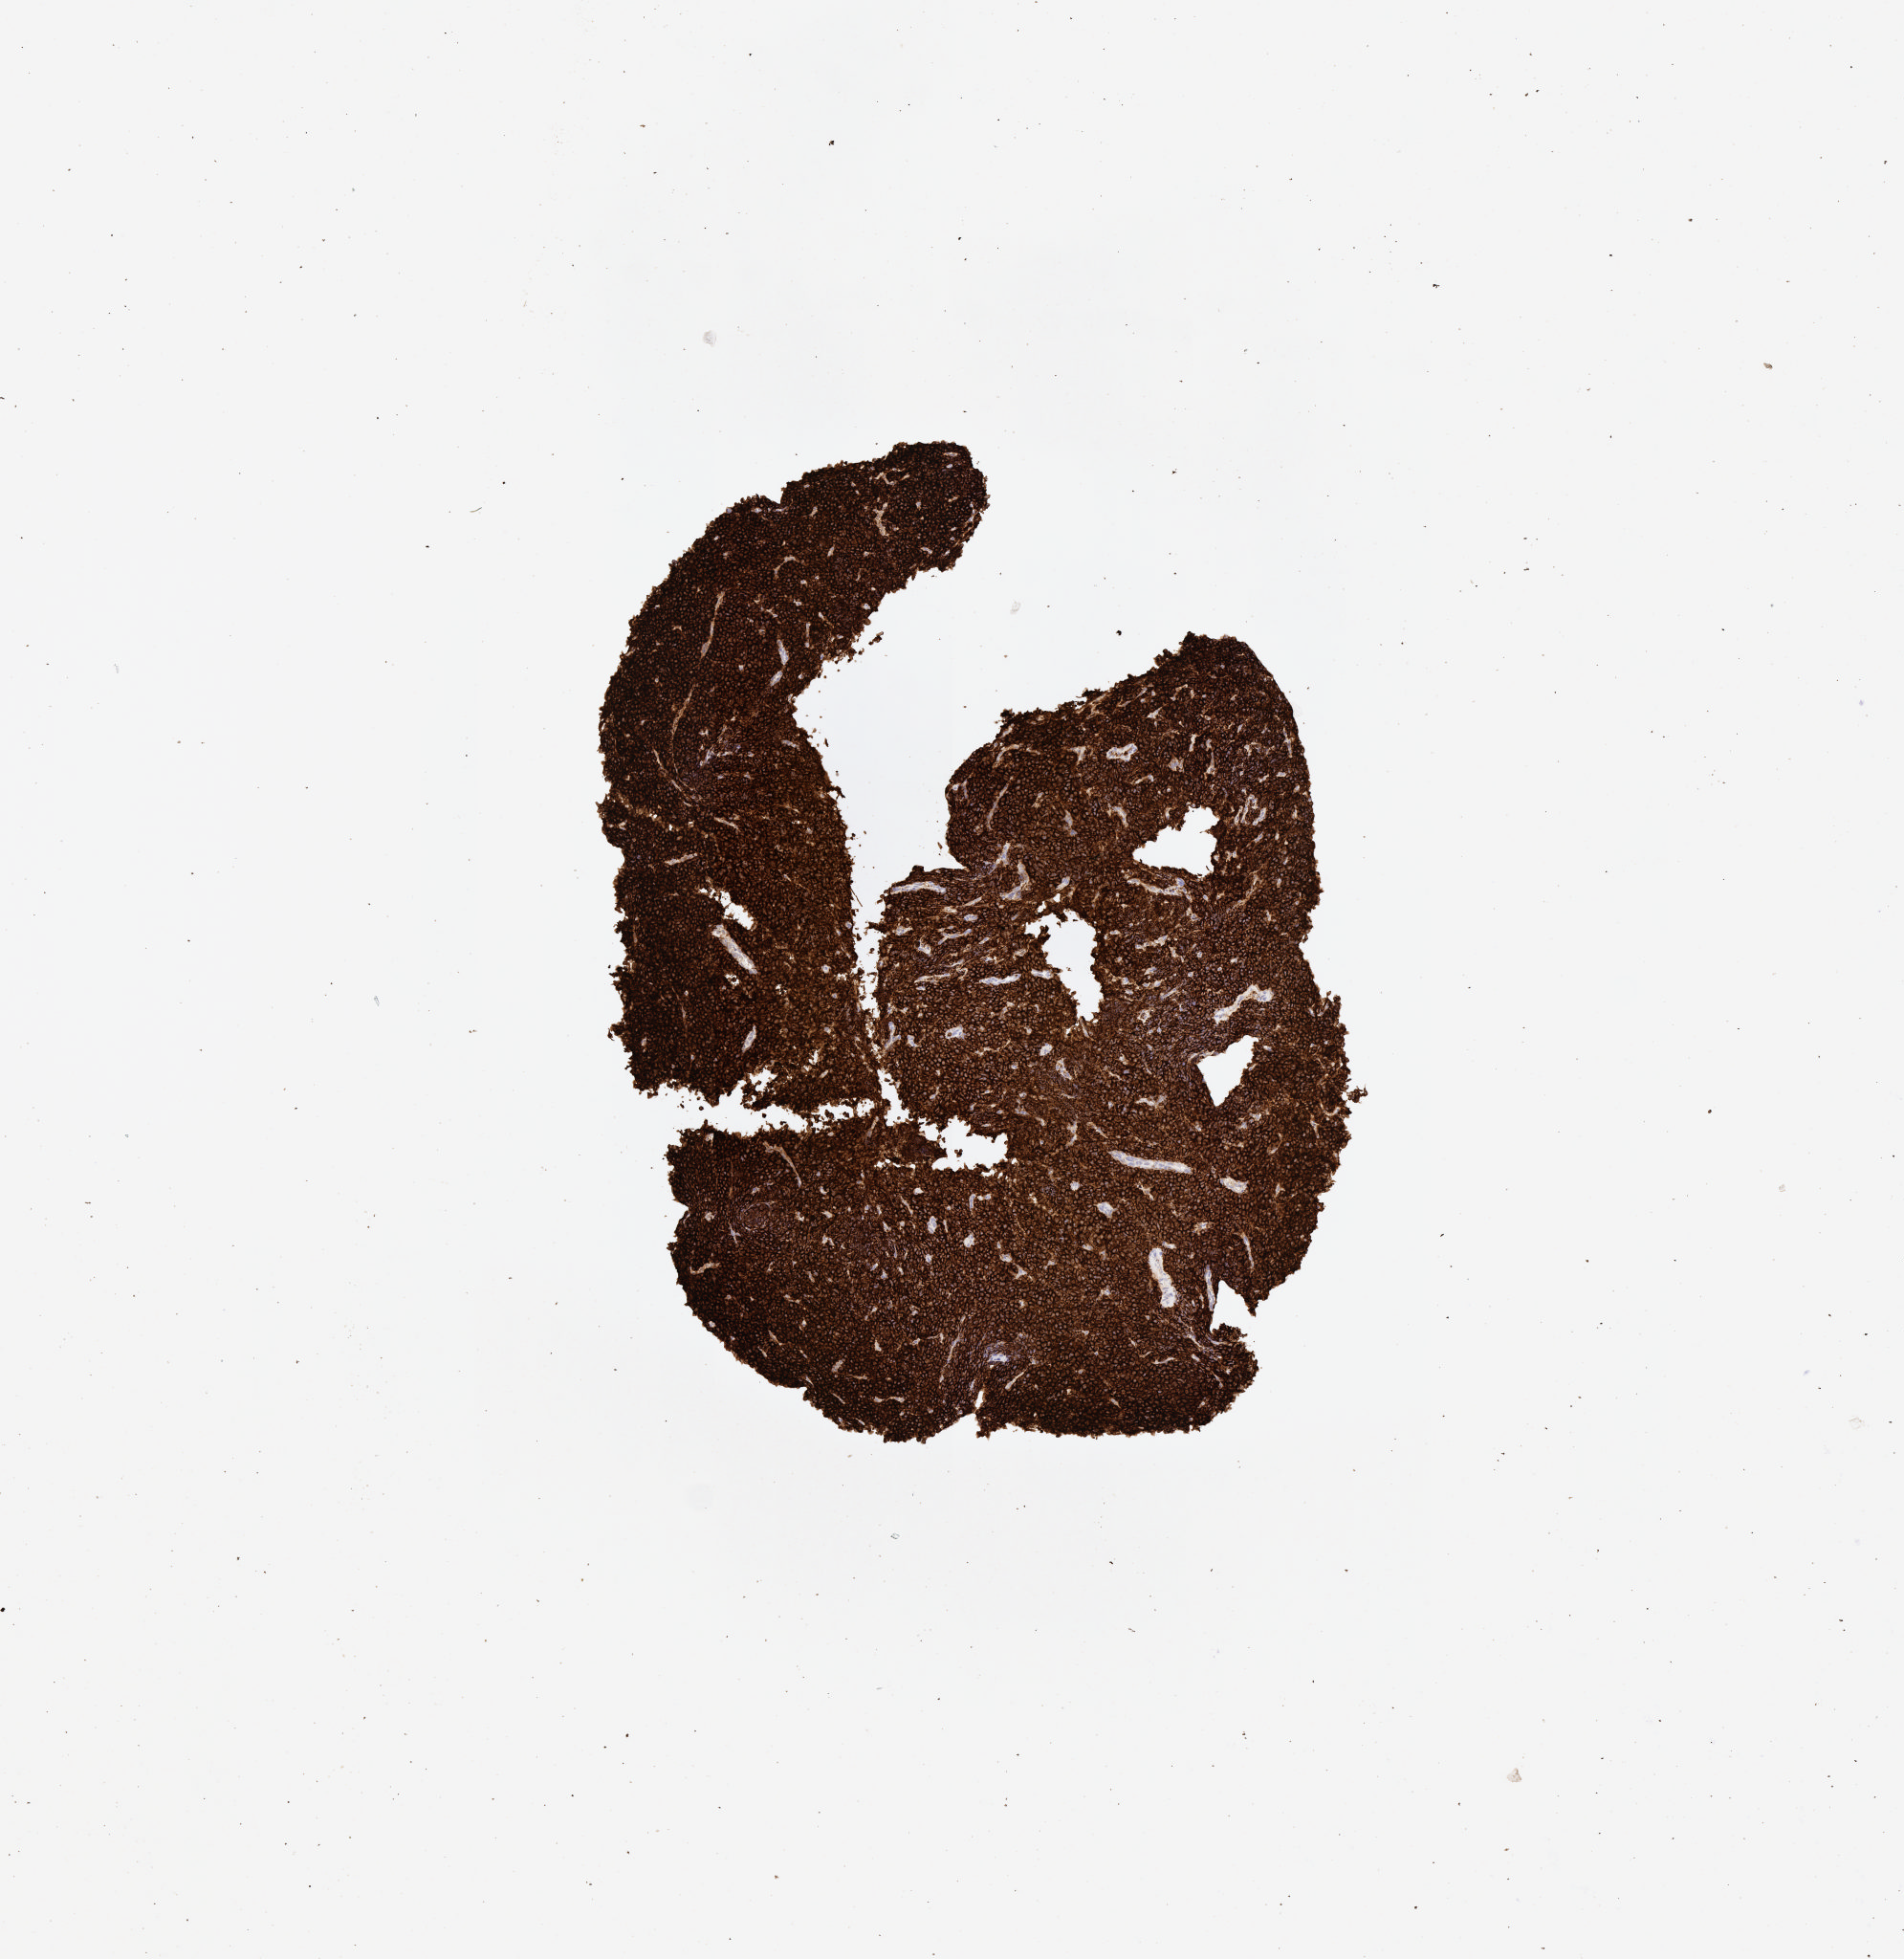
Immunohistochemistry (IHC) whole-slide image stained for CD20 — shown as a low-resolution overview of the whole scanned area (about 4.0 x 4.1 mm), specimen: tumor tissue. Patient: female, age at initial diagnosis 8 years.
- diagnosis: Burkitt lymphoma, NOS